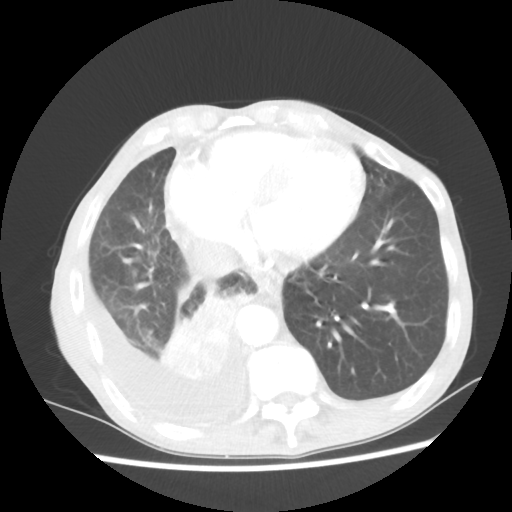
Chest CT, one axial slice. Slice 18 of 60 in the series (ordered by position). 80 kVp. Lung window (W 1500 / L -600 HU). 5 mm slice thickness. 512 × 512 image matrix, field of view 335 × 335 mm. Patient: male, 76 years. Case-level facts recorded for this patient, not image findings: clinical TNM (as recorded): T3 N3 M1a; histopathological grade: G3.
Annotated regions visible in this slice (bounding box drawn by a radiologist):
- lung tumour (recorded histology: squamous cell carcinoma): bounding box <159,286,258,382> (left, top, right, bottom; pixels)